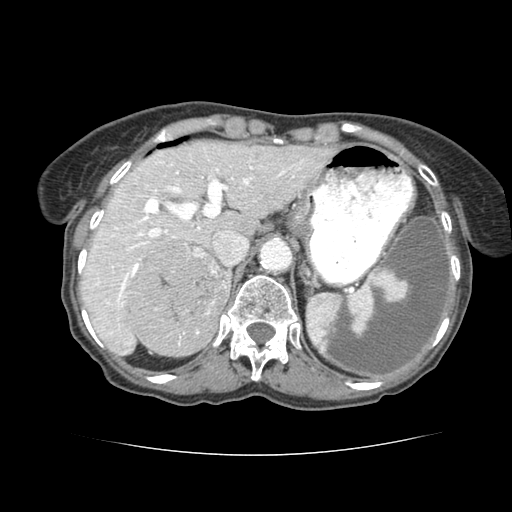
Contrast-enhanced abdominal CT (liver protocol), one axial slice; position 54 of 77 along the scan axis; 120 kVp; soft-tissue window (W 400 / L 40 HU); 2.5 mm slice thickness; 512 × 512 image matrix, field of view 340 × 340 mm. From the clinical record (not read from this slice): diagnosis: hepatocellular carcinoma (patient treated with transarterial chemoembolisation; whether this scan precedes or follows treatment is not stated here); TNM stage (as recorded): Stage-I; Child-Pugh class: A; tumour differentiation: well differentiated; tumour nodularity: uninodular.
Annotated regions visible in this slice (semi-automatically segmented with operator editing):
- liver parenchyma outside the tumour (the mass and vessels are separate outlines, so this box may not span the whole liver): box from (x=76, y=138) to (x=324, y=344) px
- mass: (x=127, y=239)–(x=227, y=354)
- liver vessels: (x=79, y=158)–(x=319, y=316)